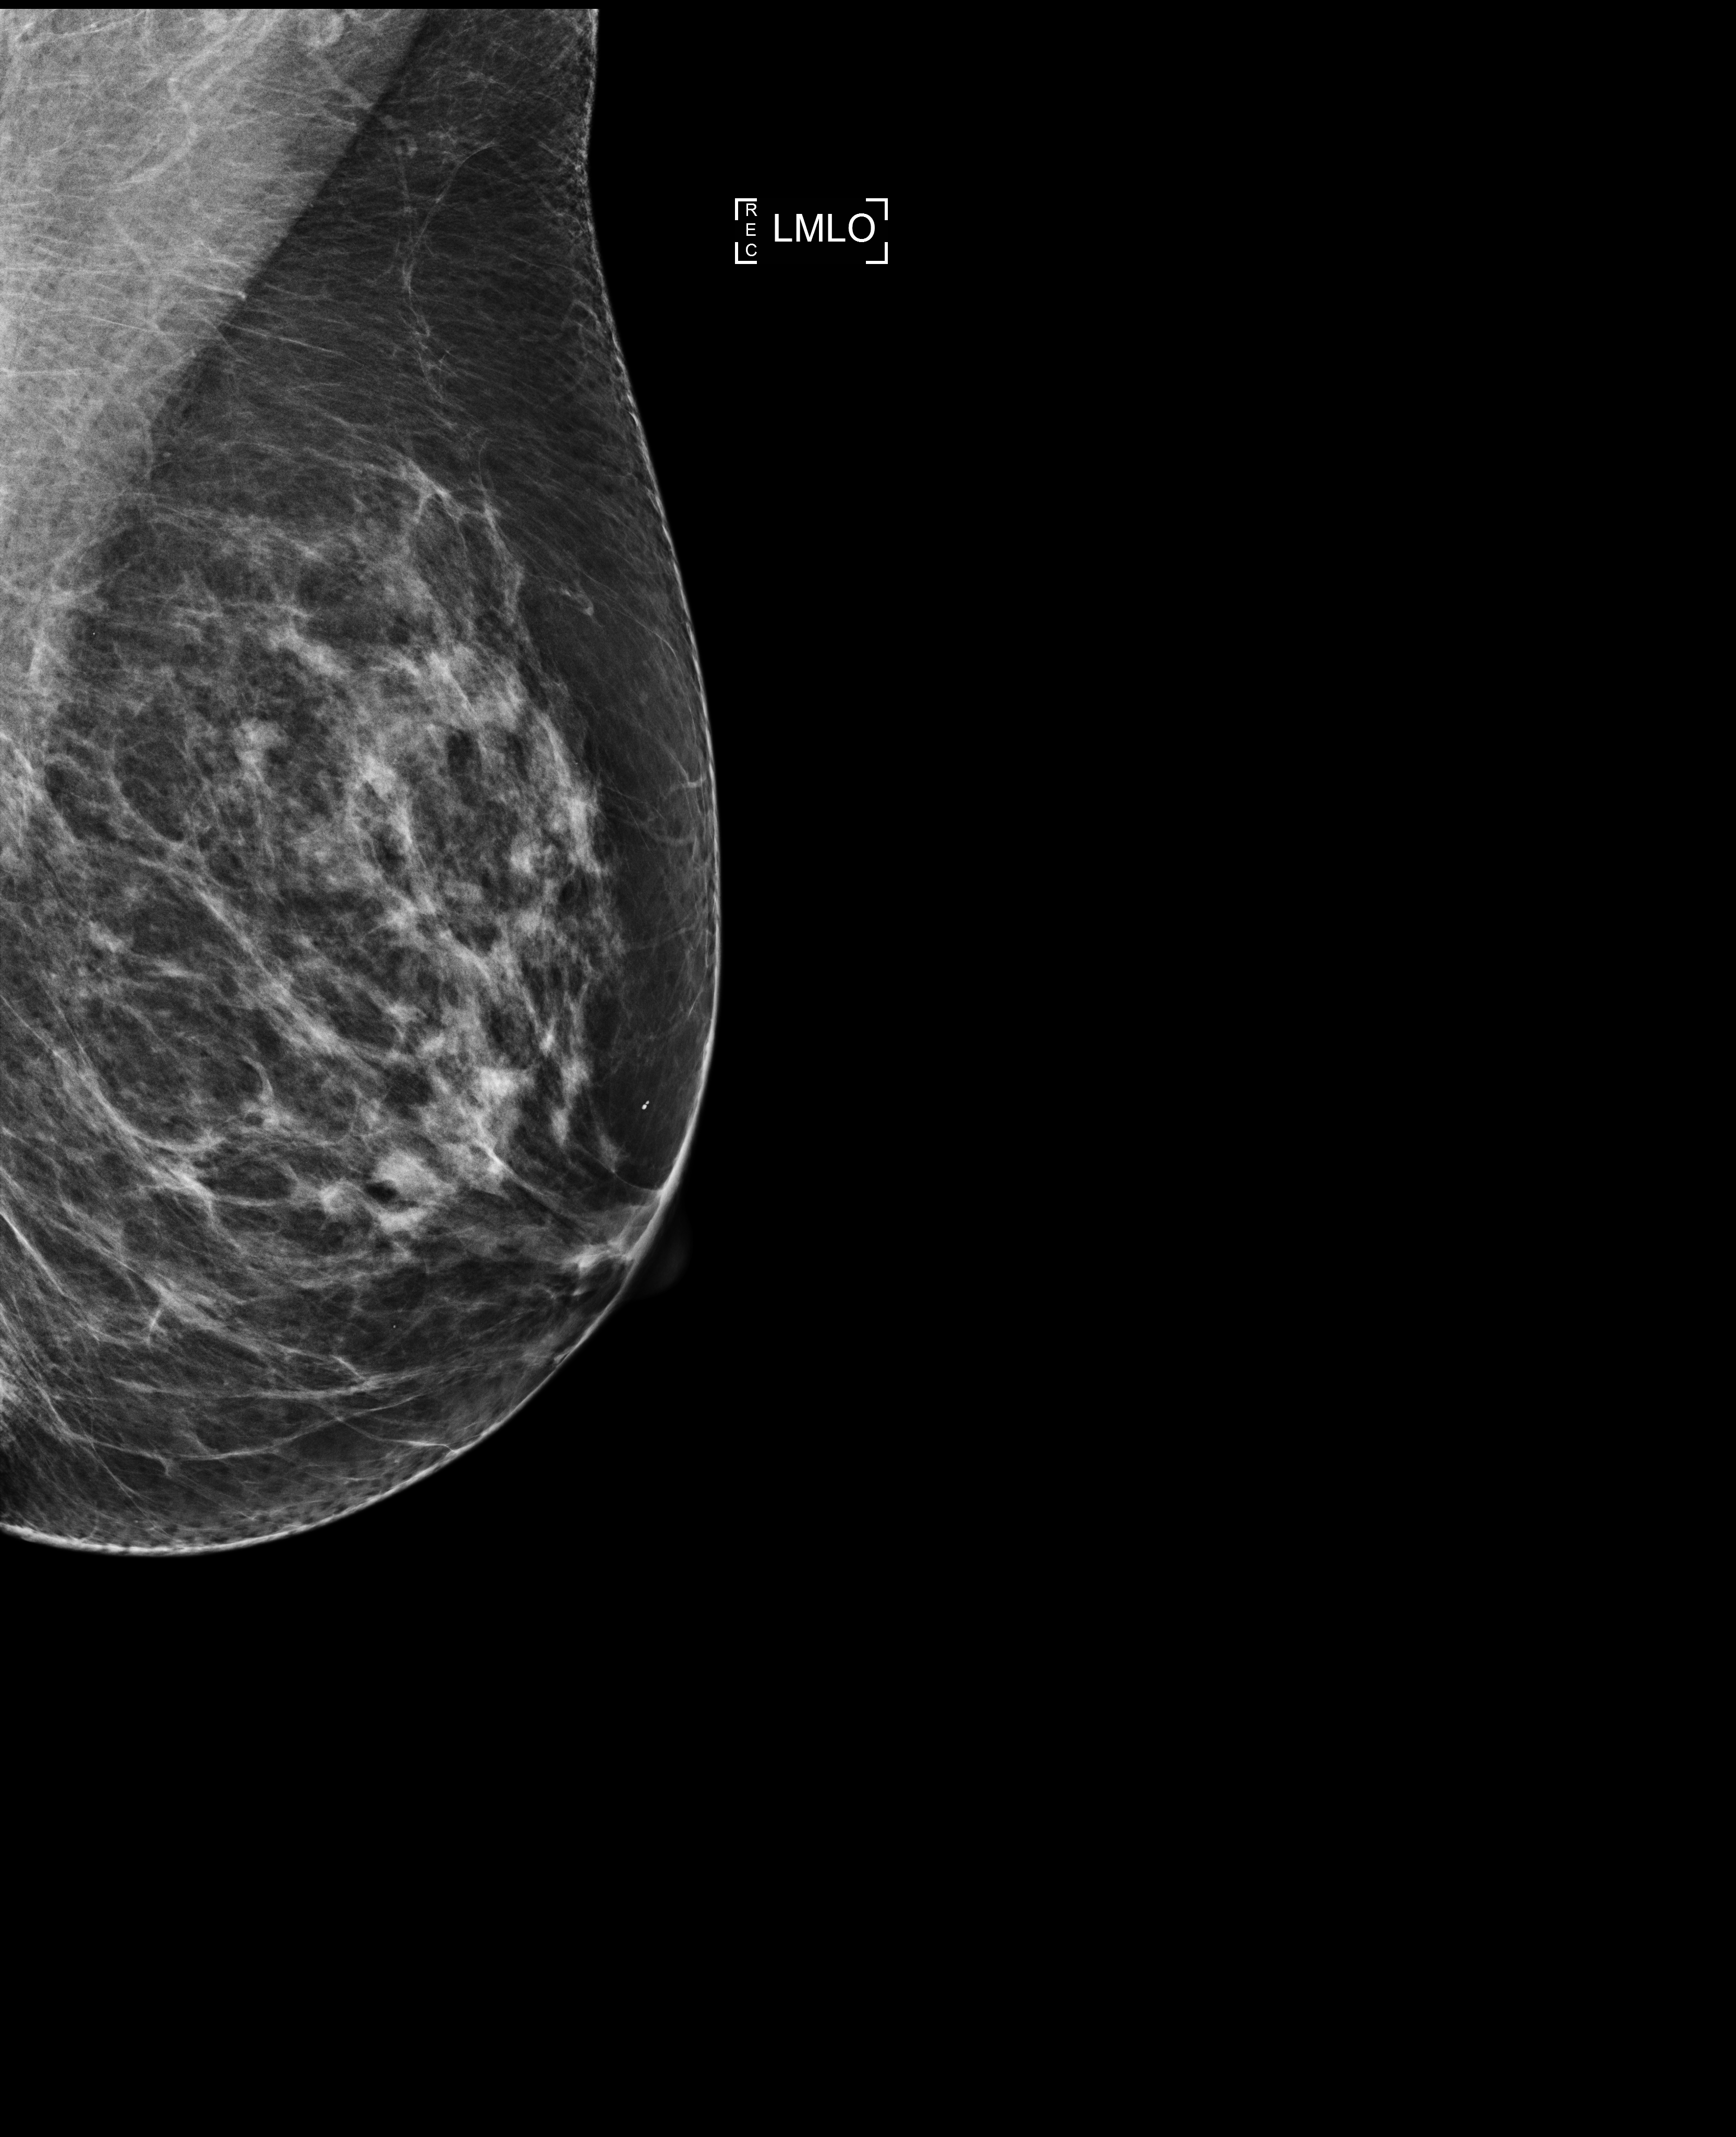
Annual screening mammography examination. Patient: female, 53 years.
Image type: full-field digital mammogram. Breast: left. Projection: MLO view.